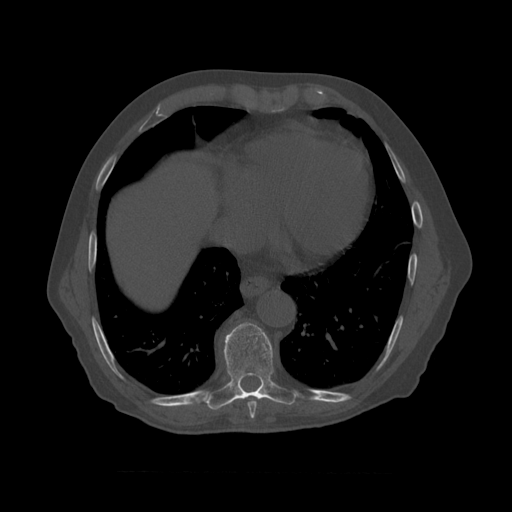
CT including the spine, one axial slice; position 450 of 450 along the scan axis; 120 kVp; bone window (W 1800 / L 400 HU); 1.25 mm slice thickness; 512 × 512 image matrix. Patient age 75 years. Case-level facts recorded for this patient, not image findings: primary cancer: prostate.
Structures marked on this image (semi-automatic segmentation, software-assisted and operator-edited):
- T8 vertebra: bounding box <220,322,300,411> (left, top, right, bottom; pixels)